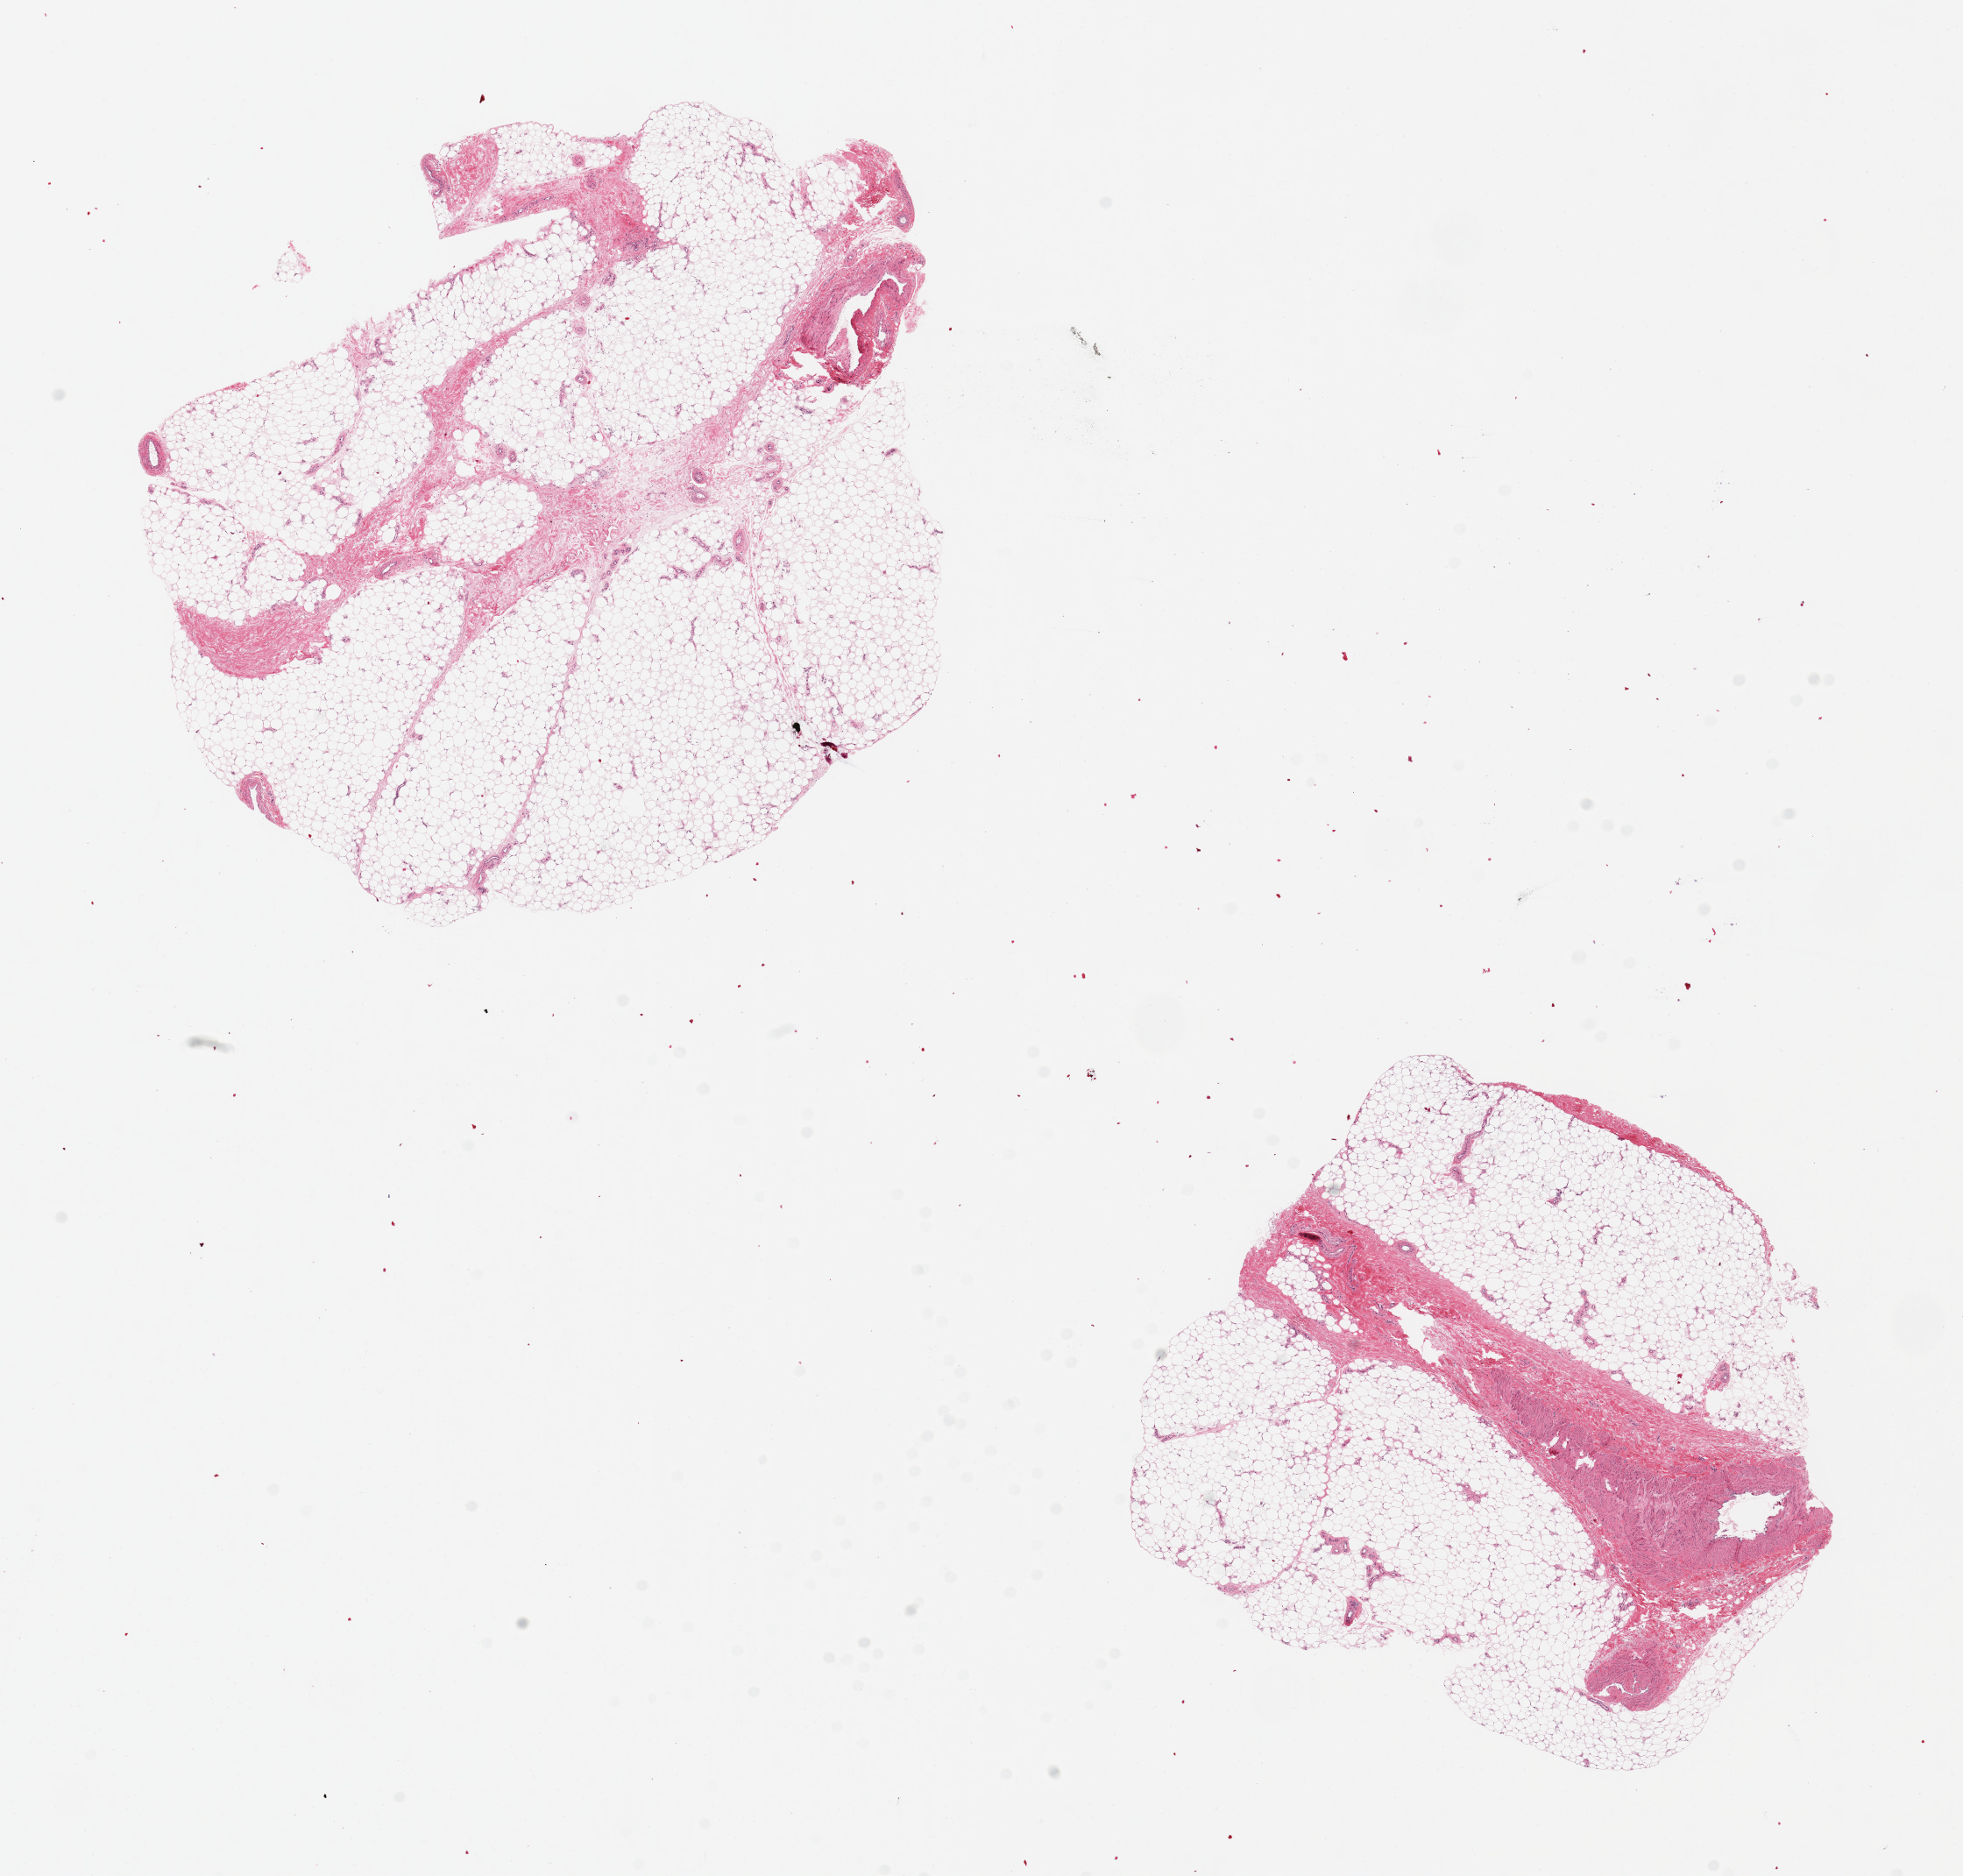
Digitized H&E-stained section, a low-resolution overview of the entire scanned area, about 17.7 x 16.9 mm (acquisition: 20x scan). PAXgene-fixed, paraffin-embedded tissue. Section of adipose tissue (target tissue). Tissue donor sample. Donor: male.
* pathologist's review note for this sample: 2 pieces, 8x7 & 6x6mm; Large vessel (5x1.5mm) runs through 1 piece